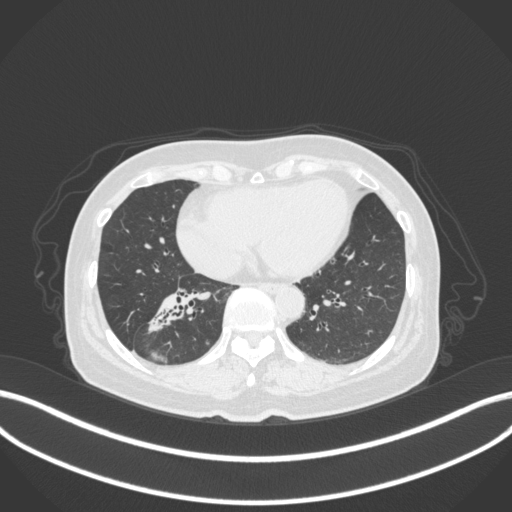
Chest CT, one axial slice. Position 141 of 429 along the scan axis. Reconstruction kernel B31f. 120 kVp. Lung window (W 1500 / L -600 HU). 1 mm slice thickness. 512 × 512 image matrix. Patient: female, 67 years. From the clinical record (not read from this slice): clinical TNM (as recorded): T1c N1 M0.
Outlined on this slice (rectangle marked by the reading radiologist):
- lung tumour (recorded histology: adenocarcinoma): bounding box [x1, y1, x2, y2] px = [147, 278, 215, 335]